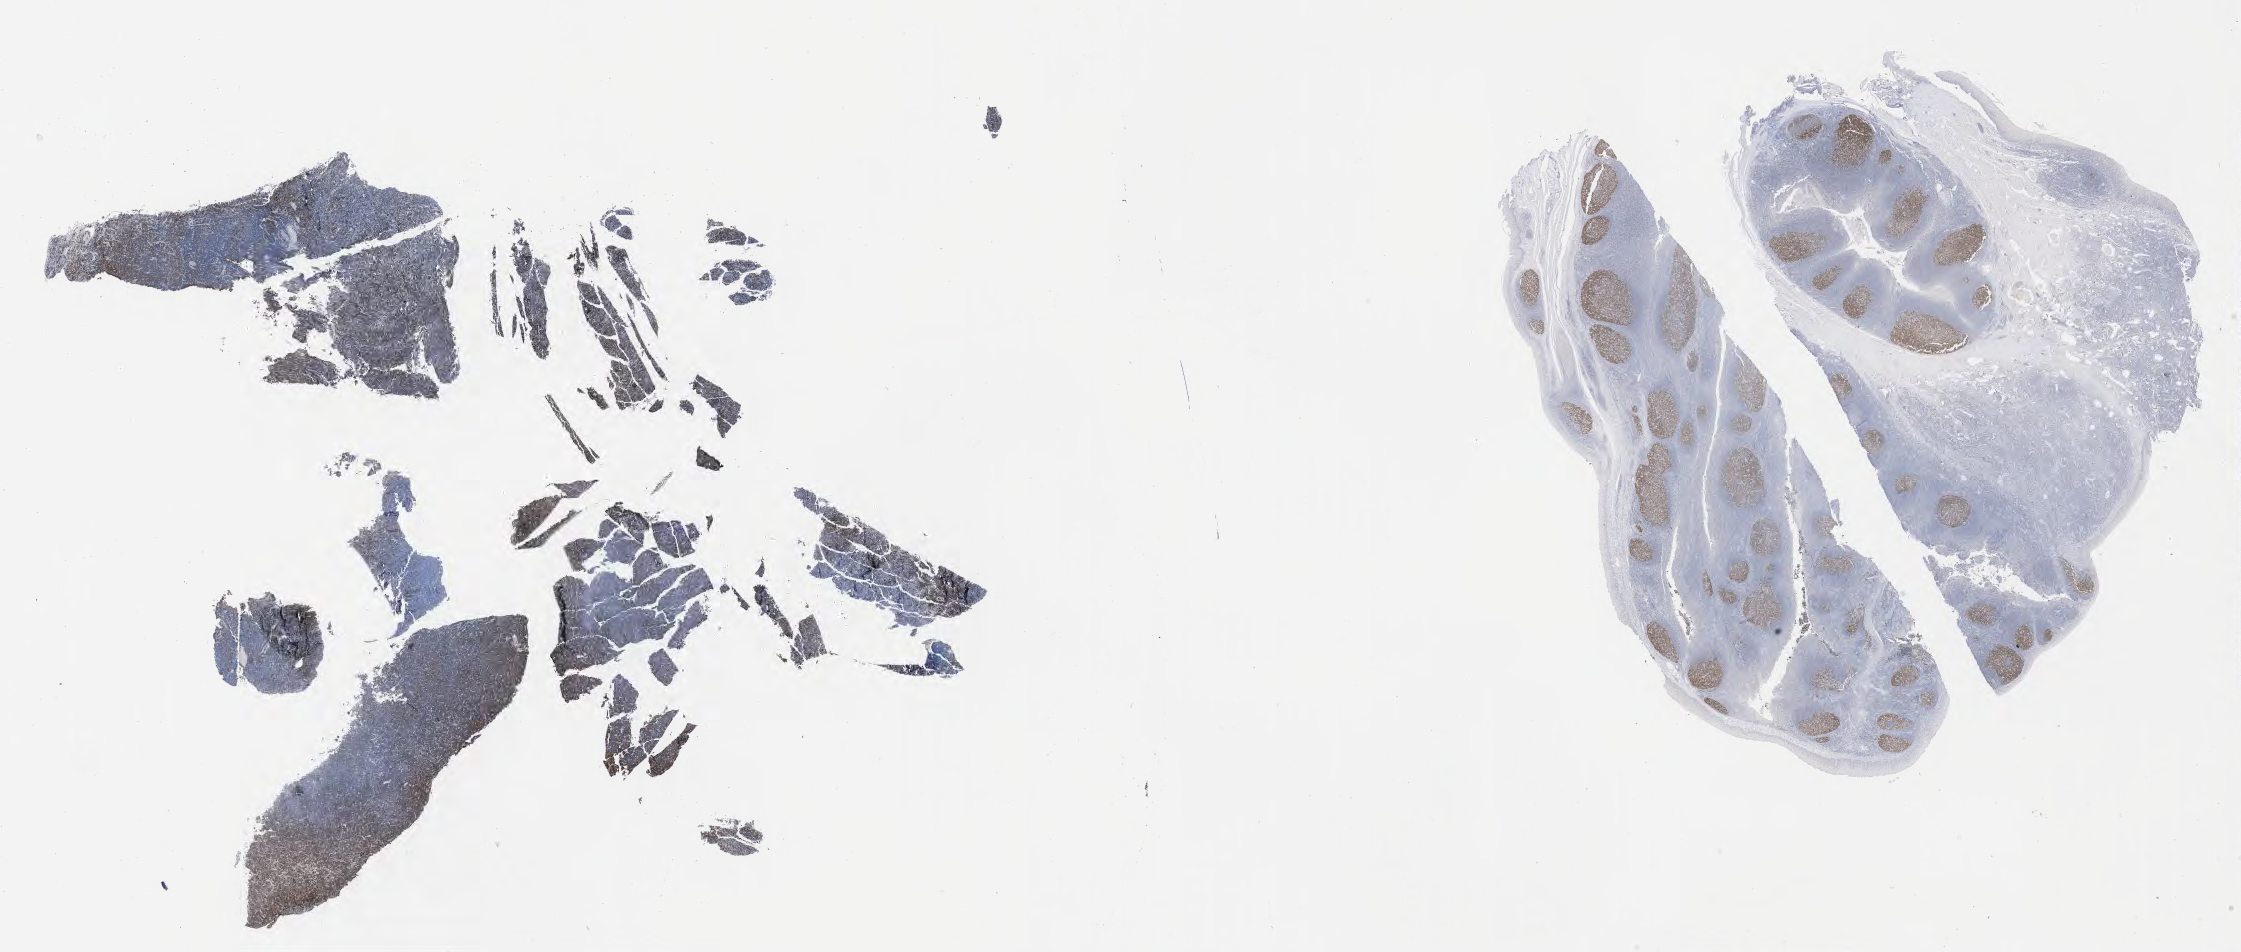
Immunohistochemistry (IHC) whole-slide image stained for BCL6 — a low-resolution overview of the entire scanned area, about 36.2 x 15.4 mm. Tumor tissue. Male patient; age at initial diagnosis 9 years.
• diagnosis: Burkitt lymphoma, NOS